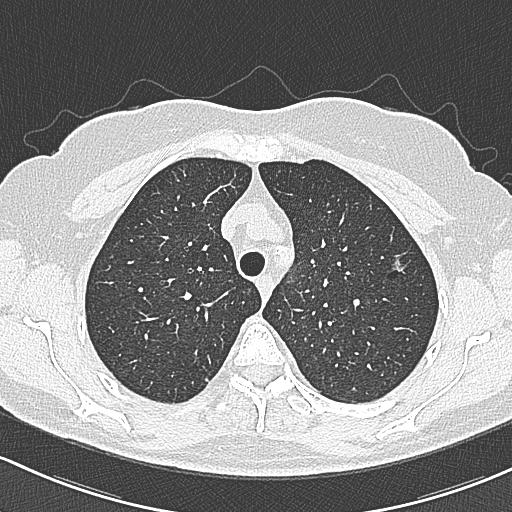
Chest CT (low-dose screening protocol), one axial image; baseline annual screen; lung window (W 1500 / L -600 HU); lung (sharp) reconstruction kernel (B80f); slice 70 of 312 in the series. Female, age 65 years at enrolment. Current smoker at enrolment.
Lesion marked by an expert reader, box from (x=377, y=243) to (x=416, y=285) px. The screening reader recorded 3 non-calcified nodules or masses ≥4 mm on this exam; which of them this box marks is not recorded. Lung cancer was diagnosed 390 days after this screen (after the second annual screen): bronchiolo-alveolar carcinoma, non-mucinous, left upper lobe, stage IA (AJCC 6th edition), 10 mm at pathology.